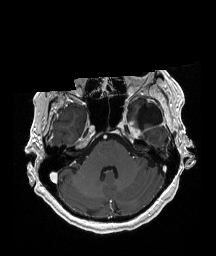
Brain MRI from a brain-tumour surgery series, one axial slice; slice 140 of 192 in the series (ordered by position); T1-weighted post-contrast; 1 mm slice thickness; 216 × 256 image matrix, field of view 211 × 250 mm. Case-level facts recorded for this patient, not image findings: histopathology: Glioblastoma; WHO grade: 4; IDH mutation: no; tumour location: Left Temporal.
Outlined on this slice (expert manual segmentation):
- previous resection cavity: bounding box [x1, y1, x2, y2] px = [136, 104, 162, 129]